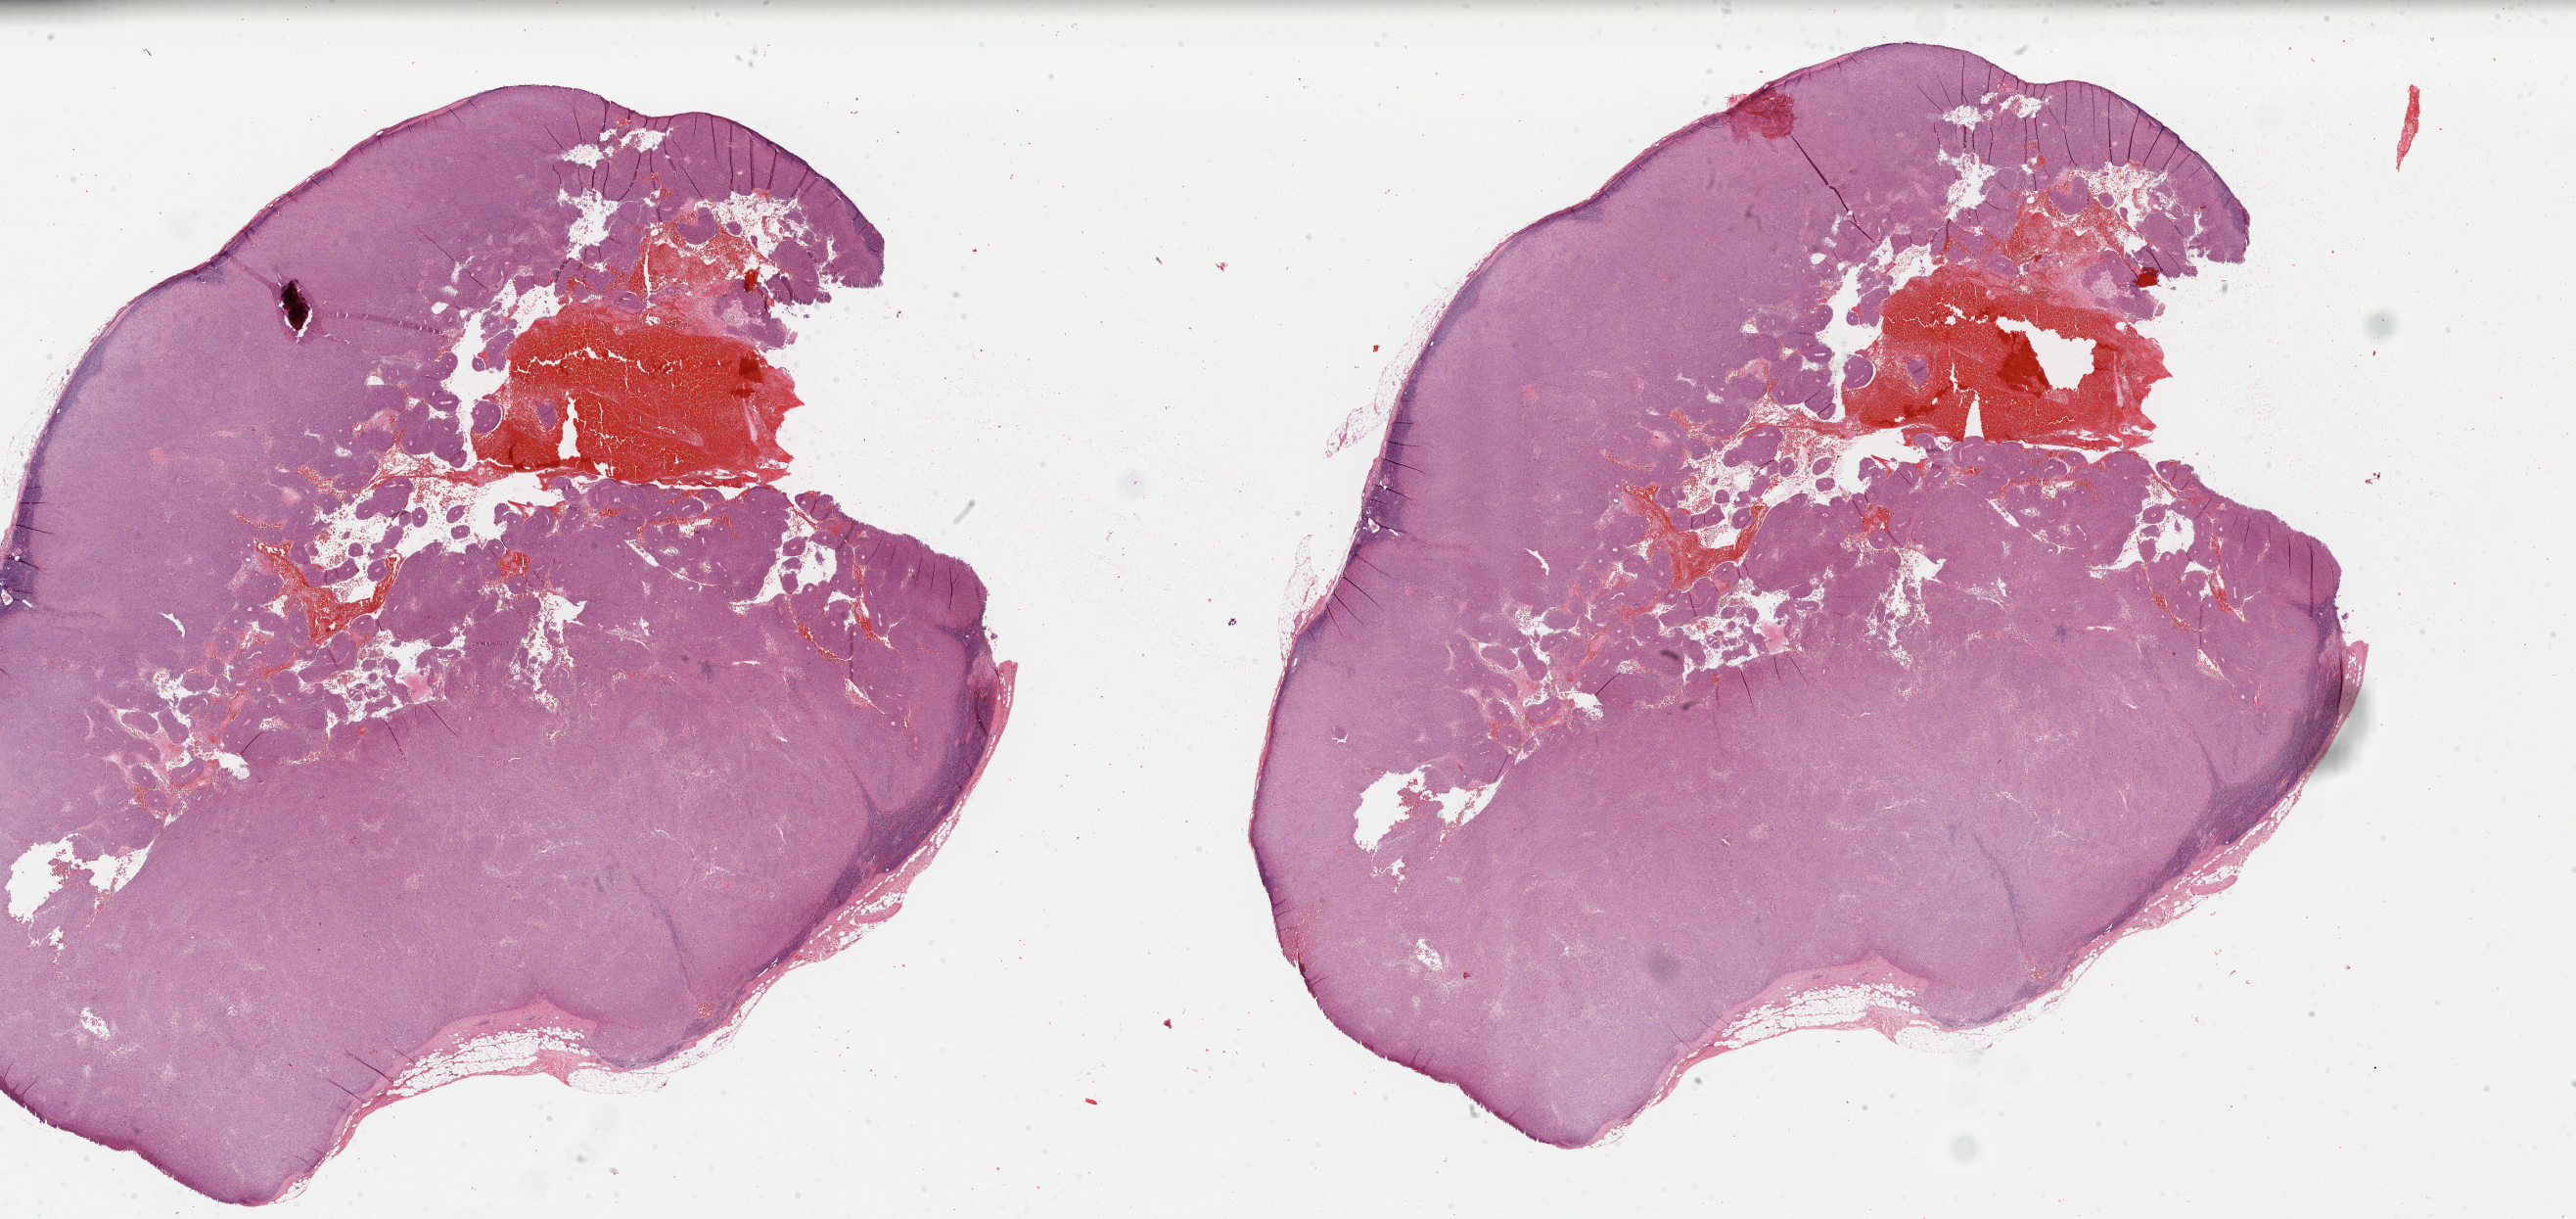
Digitized H&E tissue section (whole slide) — a low-resolution overview of the entire scanned area, about 41.5 x 19.6 mm (slide scanned at 40x). FFPE section. Metastatic tumour sample, sampled site not recorded. Patient: male, age at initial diagnosis 73 years.
This section: metastatic tumour tissue. Patient diagnosis: Malignant melanoma, NOS.